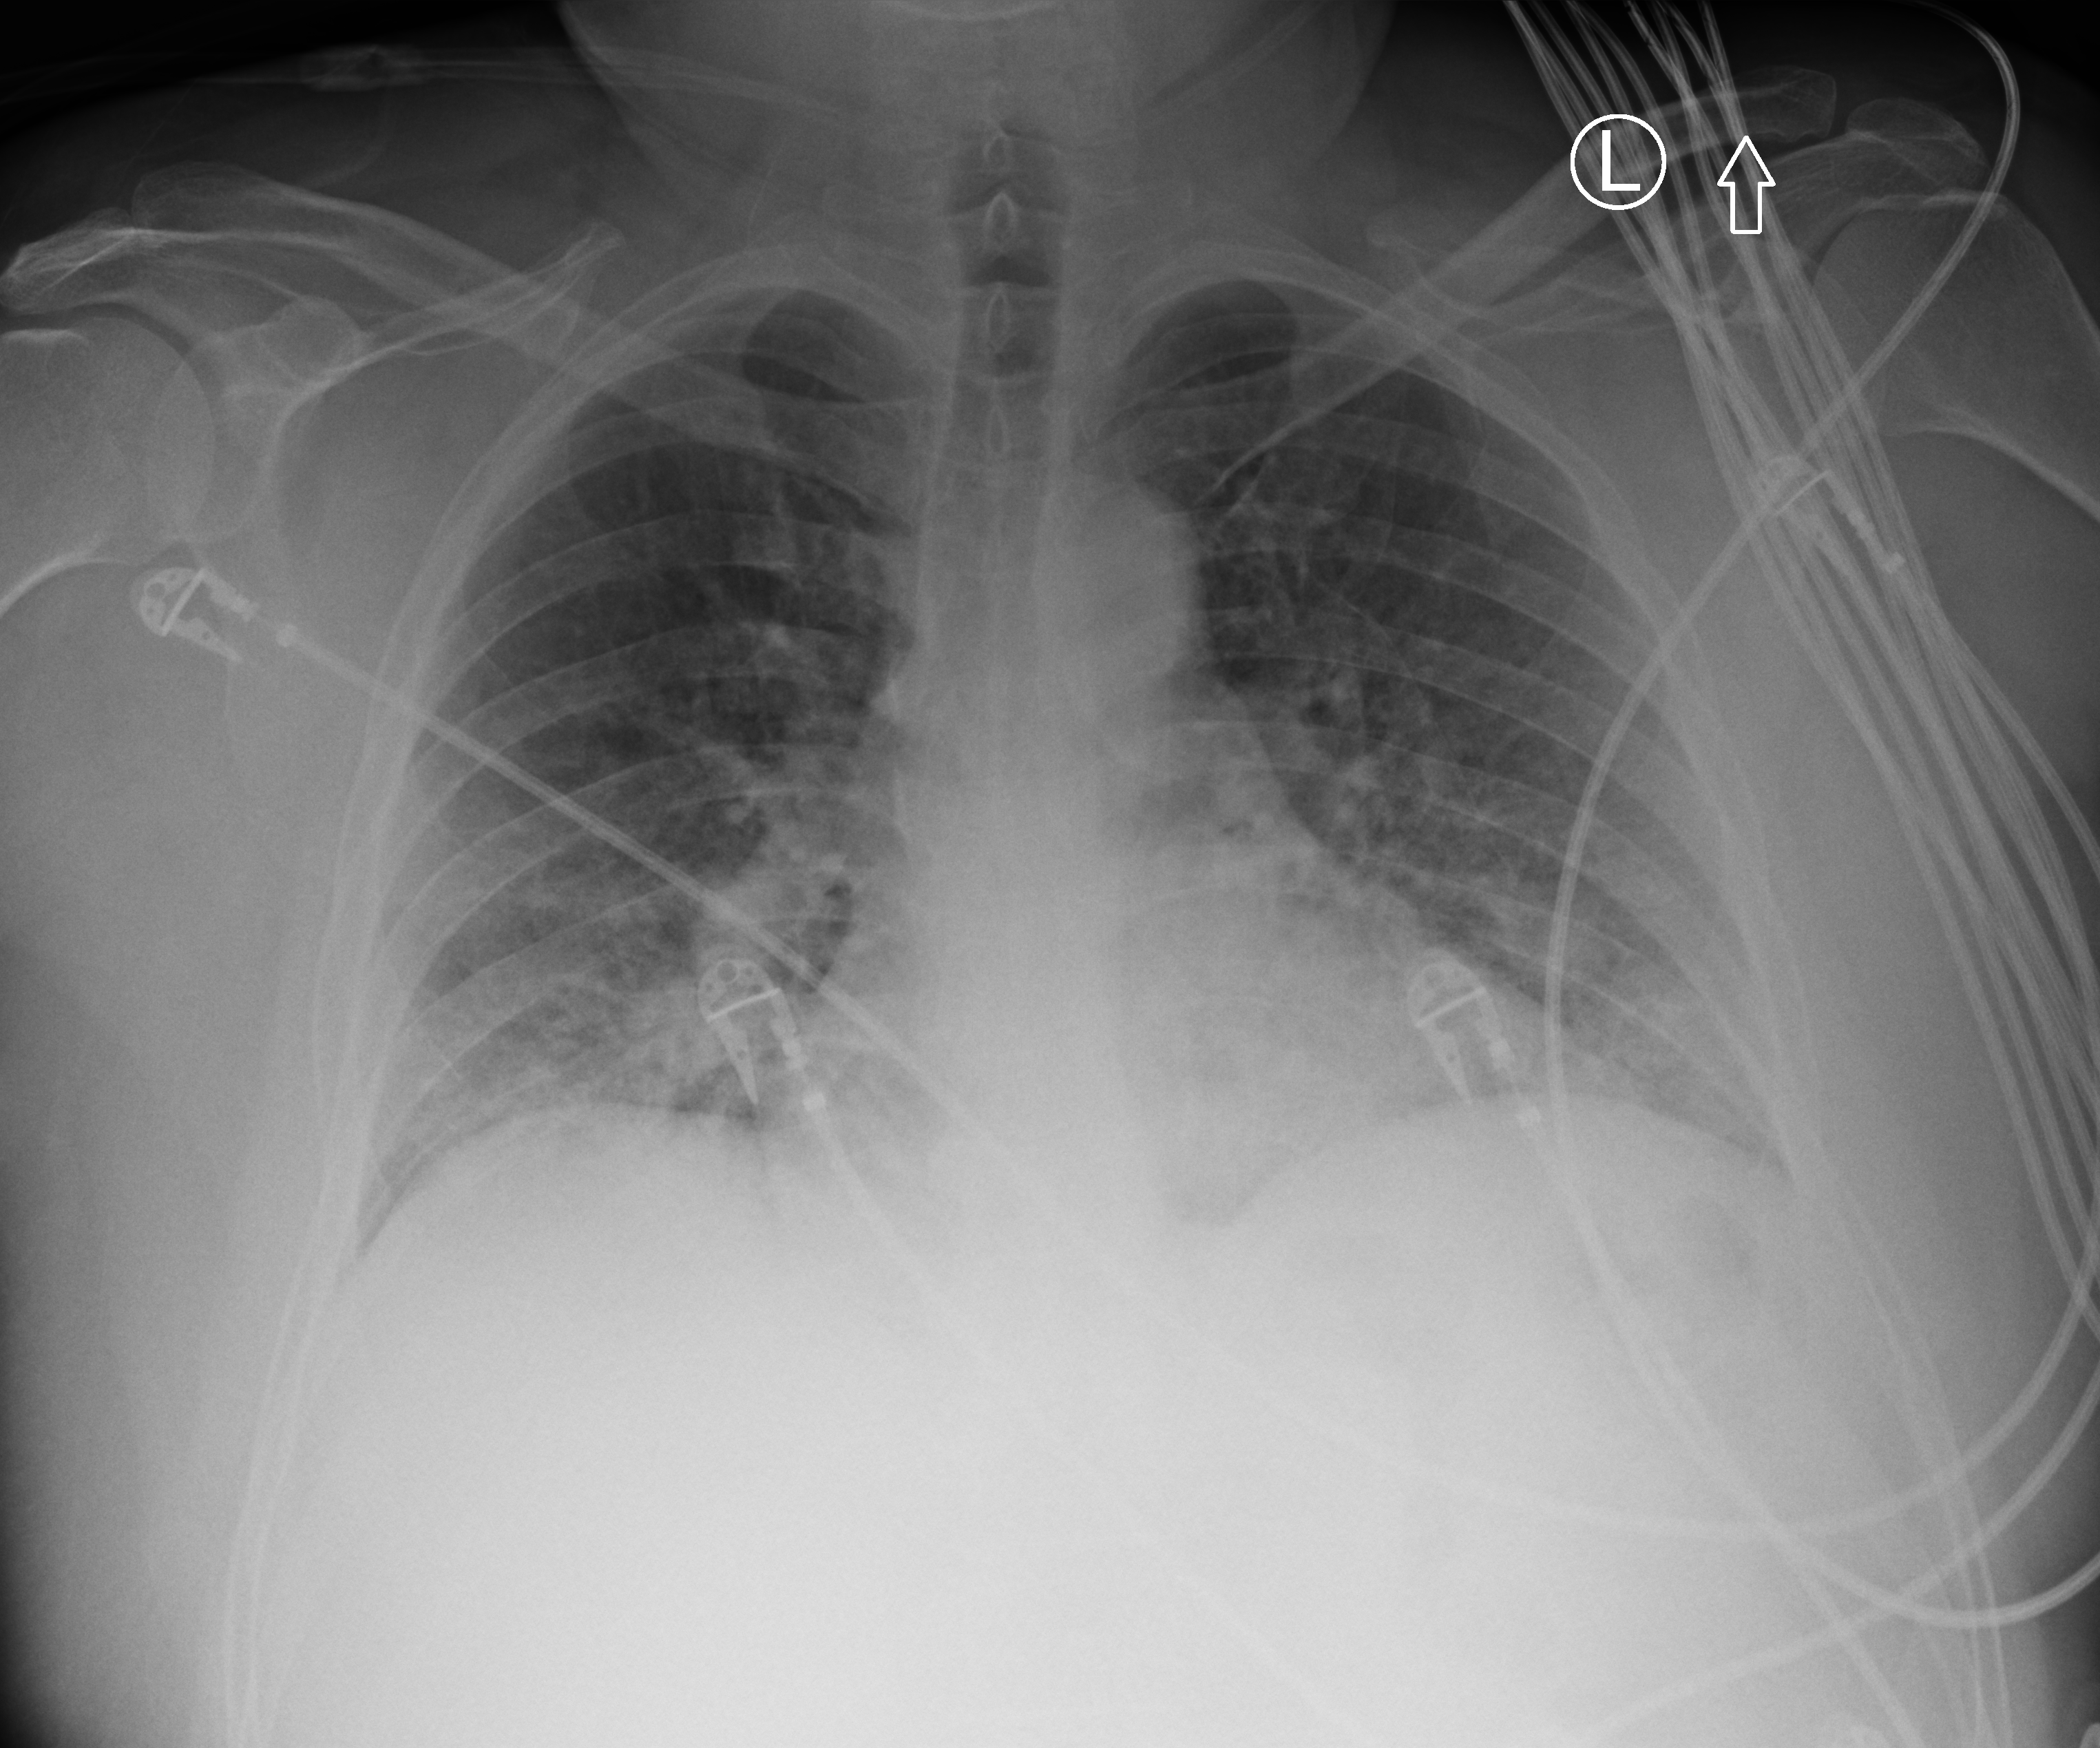
Portable chest radiograph; anteroposterior (AP) projection. Patient hospitalised with COVID-19; male, aged 18–59 years.
Hospital-stay facts (about this admission, not read from this image; timing relative to this image not recorded): chronic kidney disease (admission record): no.